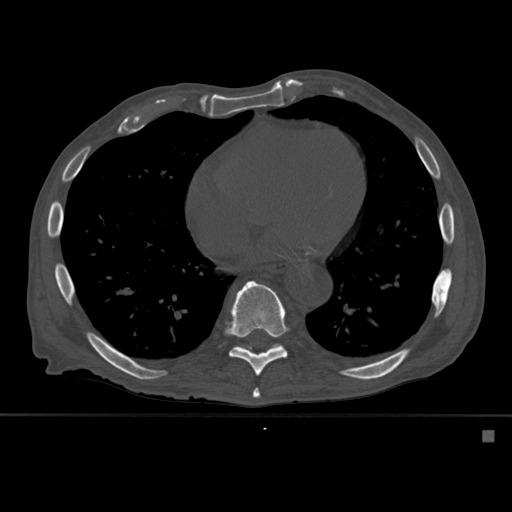
CT including the spine, one axial slice; bone window (W 1800 / L 400 HU); 512 × 512 image matrix, field of view 373 × 373 mm. Patient: male, 78 years. Case-level facts recorded for this patient, not image findings: primary cancer: prostate.
Structures marked on this image (semi-automatically segmented with operator editing):
- T10 vertebra: box from (x=270, y=345) to (x=276, y=349) px
- T8 vertebra: (x=252, y=388)–(x=260, y=398)
- T9 vertebra: (x=225, y=280)–(x=290, y=376)